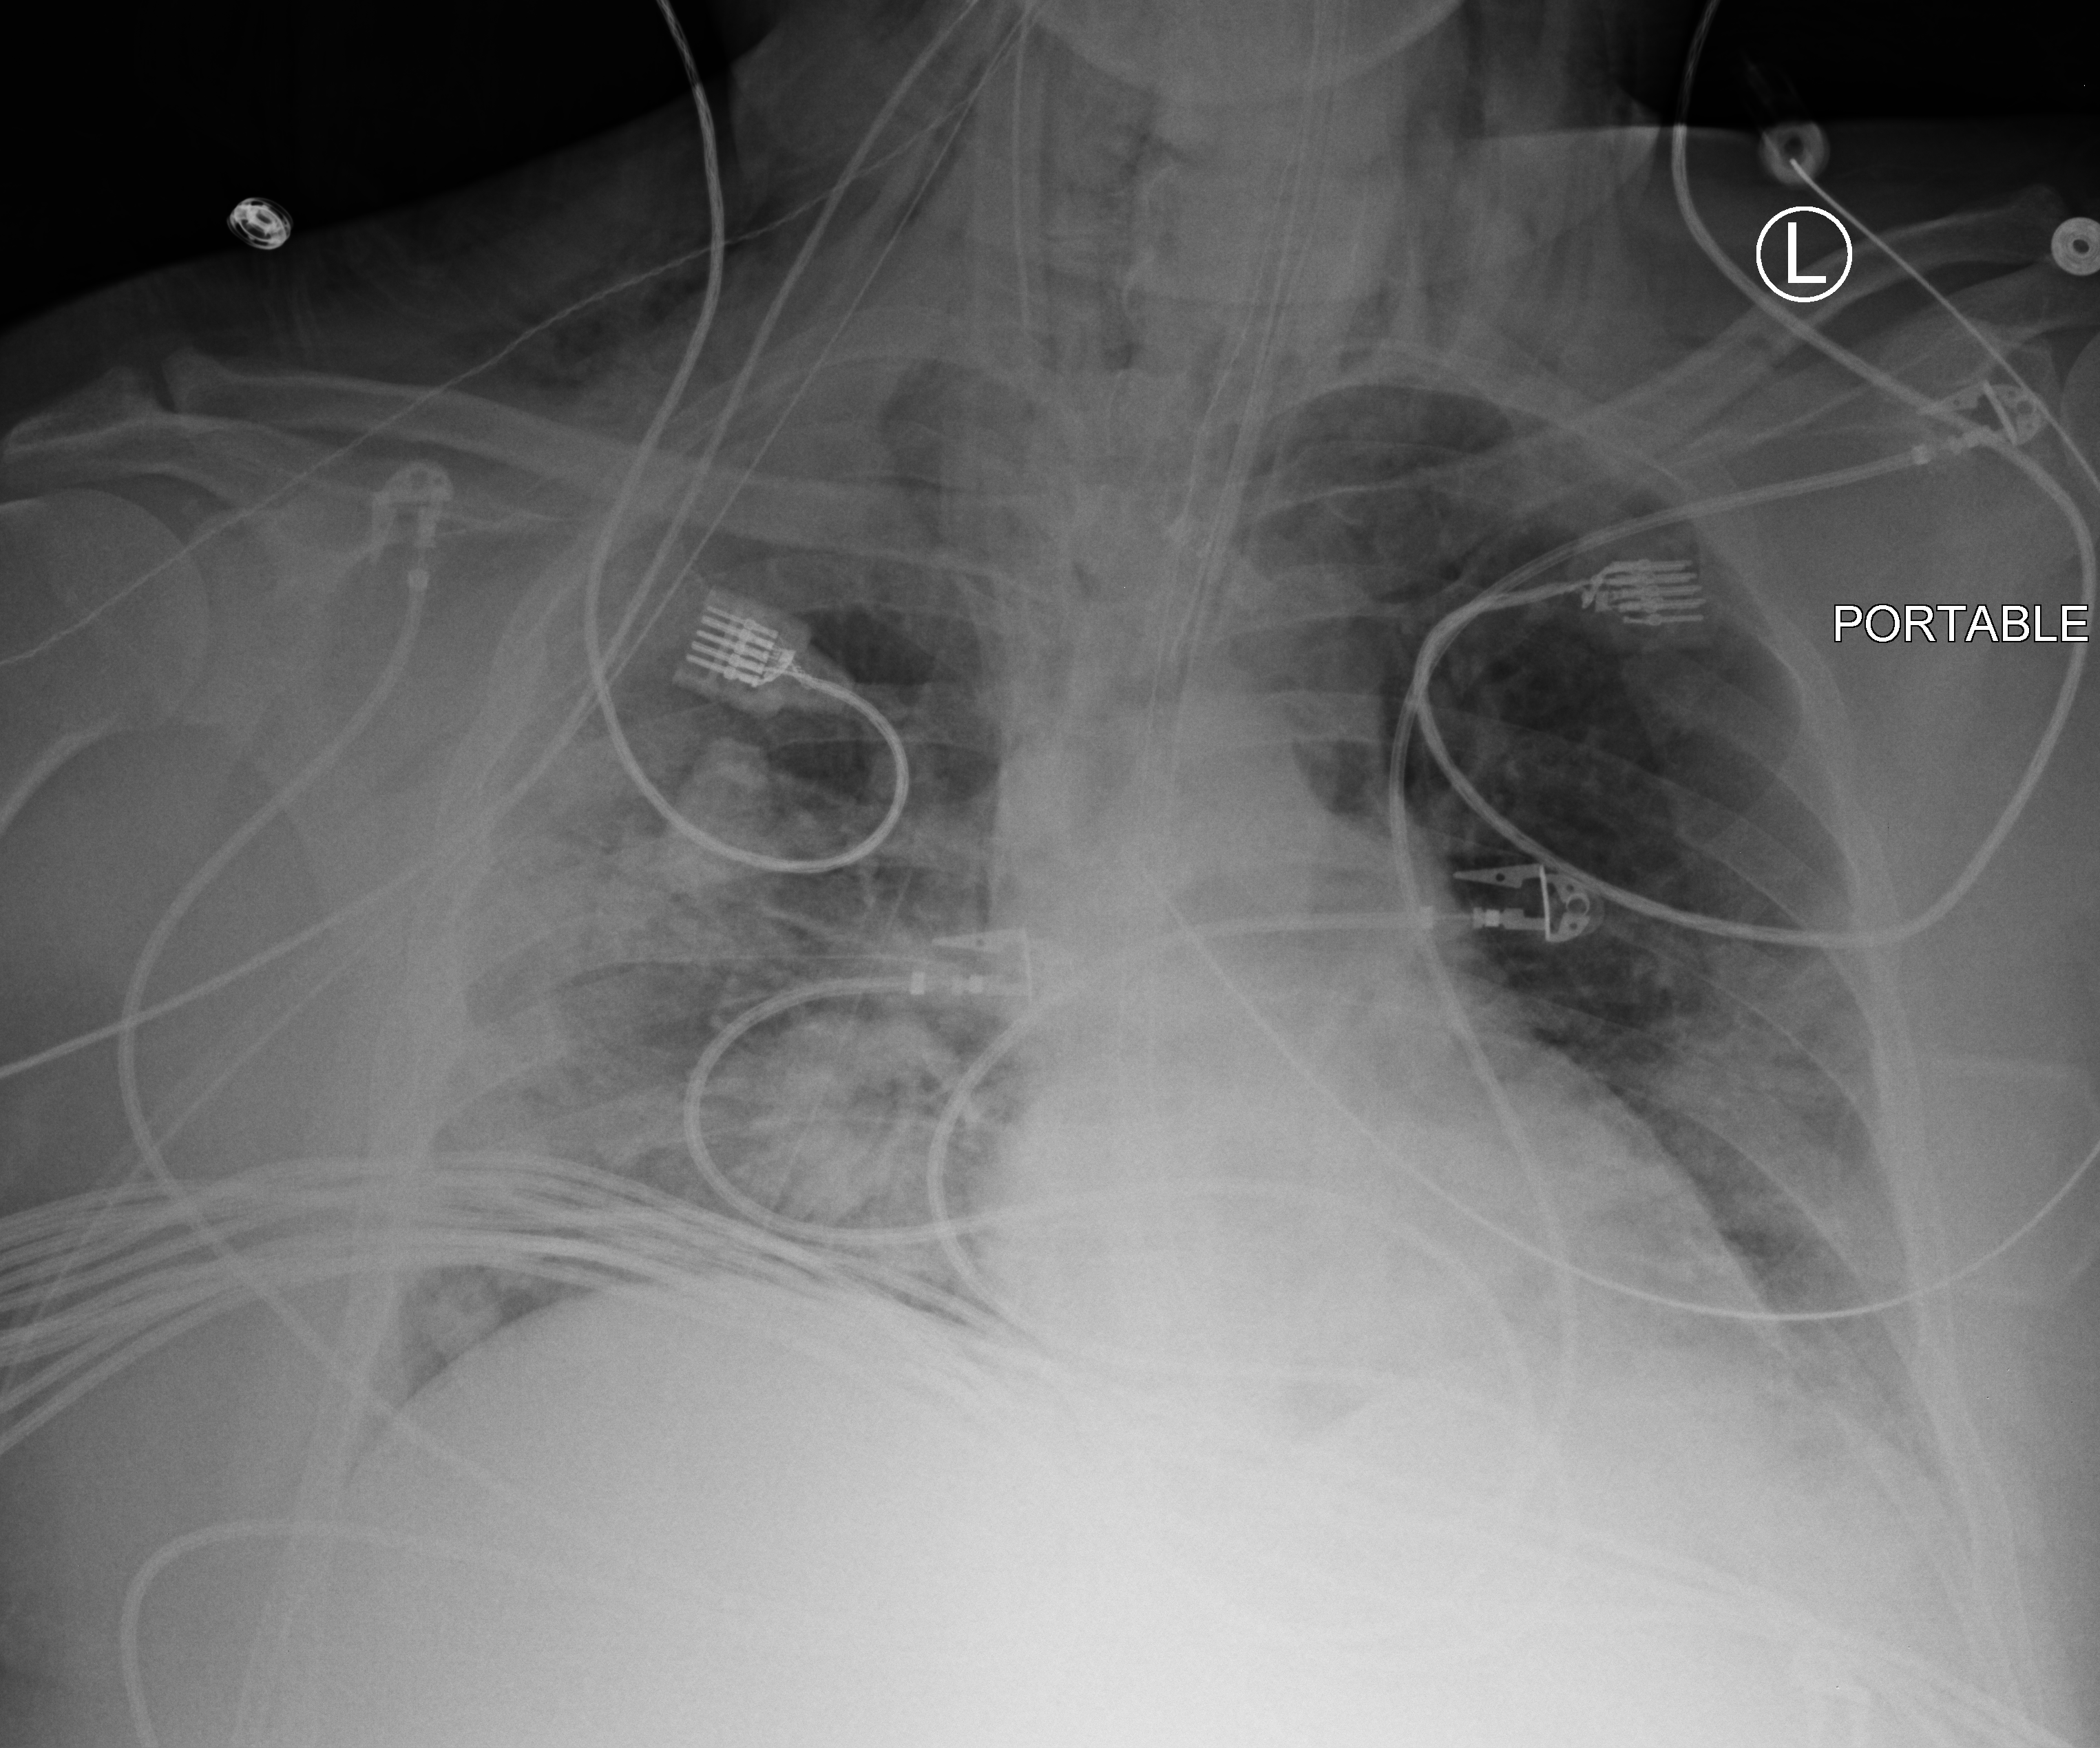
Chest X-ray (portable), anteroposterior (AP) projection. Patient hospitalised with COVID-19, aged 18–59 years.
Admission-level facts for this patient (not findings on this image; timing relative to this image not recorded):
- mechanically ventilated during this hospital stay: yes
- admitted to intensive care during this hospital stay: yes
- chronic kidney disease (admission record): no